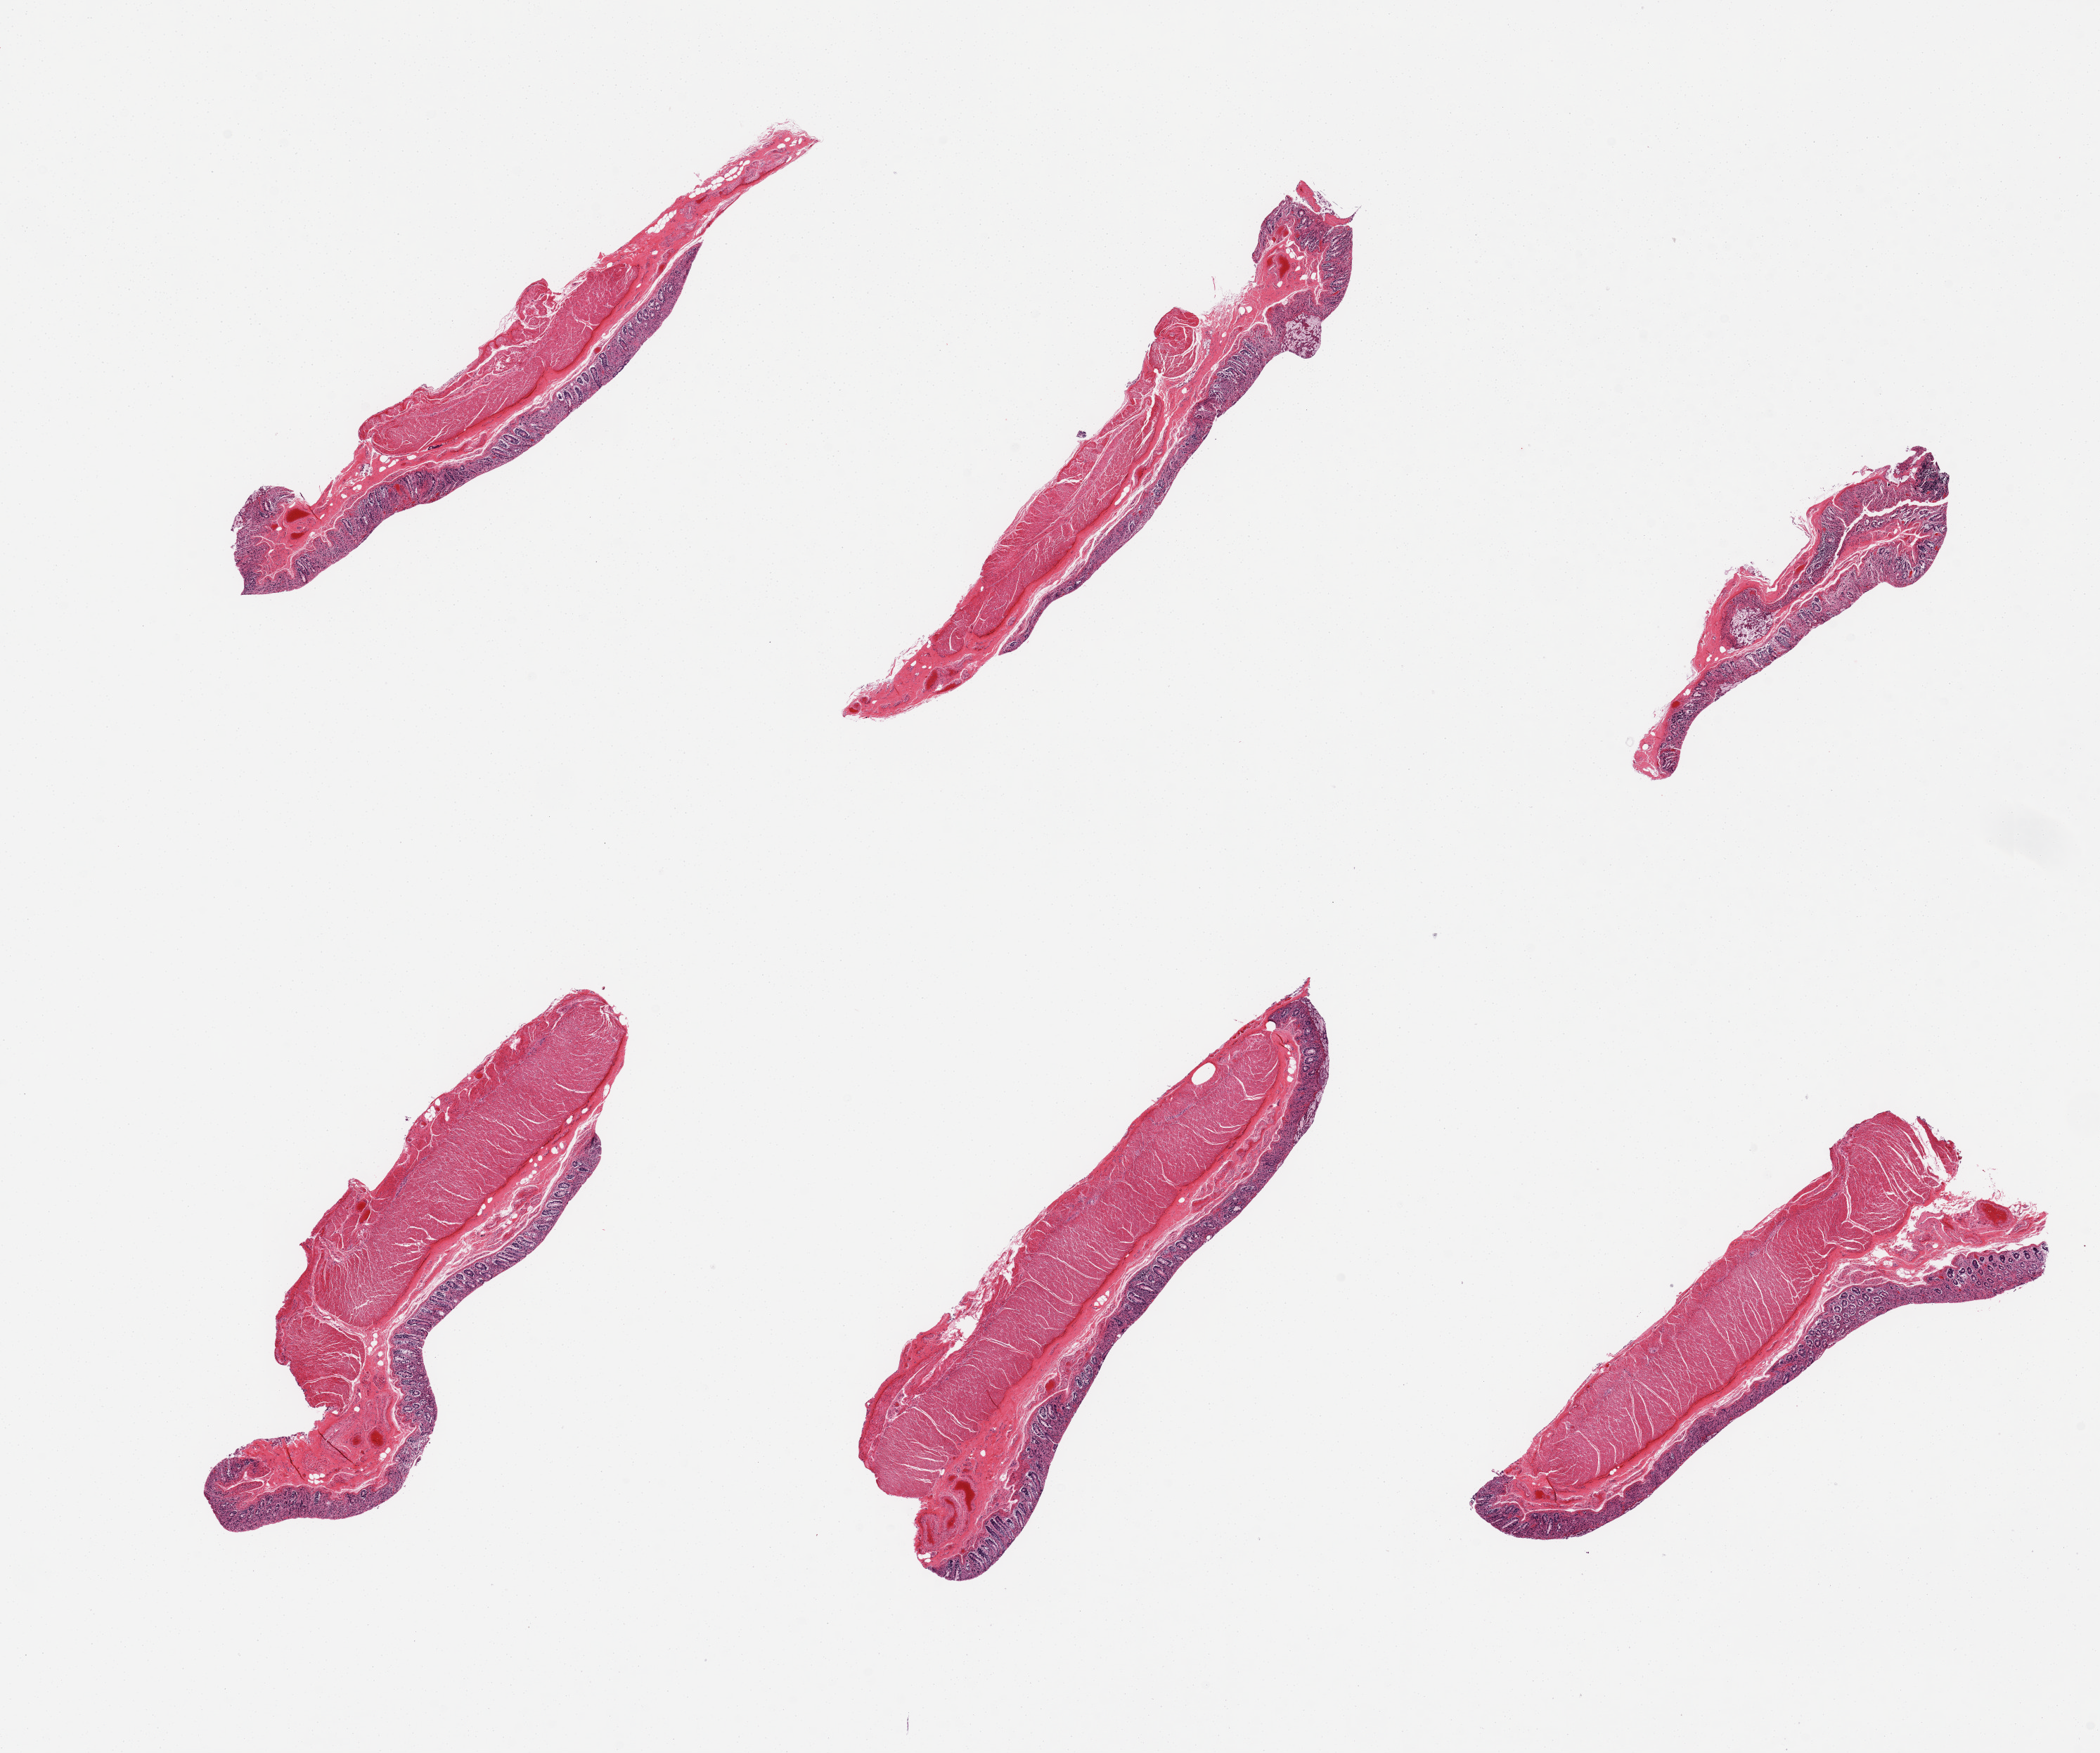
Digitized H&E-stained section, shown as a low-resolution overview of the whole scanned area (about 23.6 x 19.7 mm, acquisition: 20x scan), PAXgene-fixed, paraffin-embedded tissue, section of transverse colon (target tissue), donor tissue sample.
Pathologist's review note for this sample: 6 pieces, epithelial component of mucosa completely sloughed, some lamina propria elements remain.